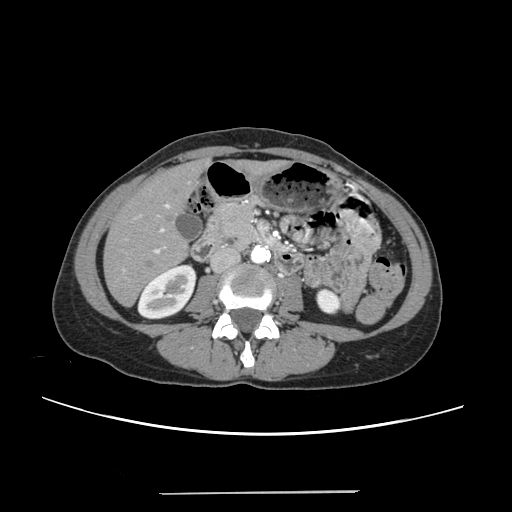
Contrast-enhanced abdominal CT, one axial slice. Slice 84 of 240 in the series (ordered by position). 120 kVp. Soft-tissue window (W 400 / L 40 HU). 512 × 512 image matrix. Female patient, age 60 years. Case-level facts recorded for this patient, not image findings: diagnosis: colorectal cancer liver metastases, imaged before liver resection; multiple liver metastases: no; largest metastasis: 1.5 cm; disease in both lobes: no.
Outlined on this slice (outlined manually by an expert reader):
- liver: bounding box [x1, y1, x2, y2] px = [105, 163, 268, 305]
- planned liver remnant (the part of the liver to remain after resection): [105, 166, 271, 304]
- portal vein (with intrahepatic branches): [123, 204, 169, 270]